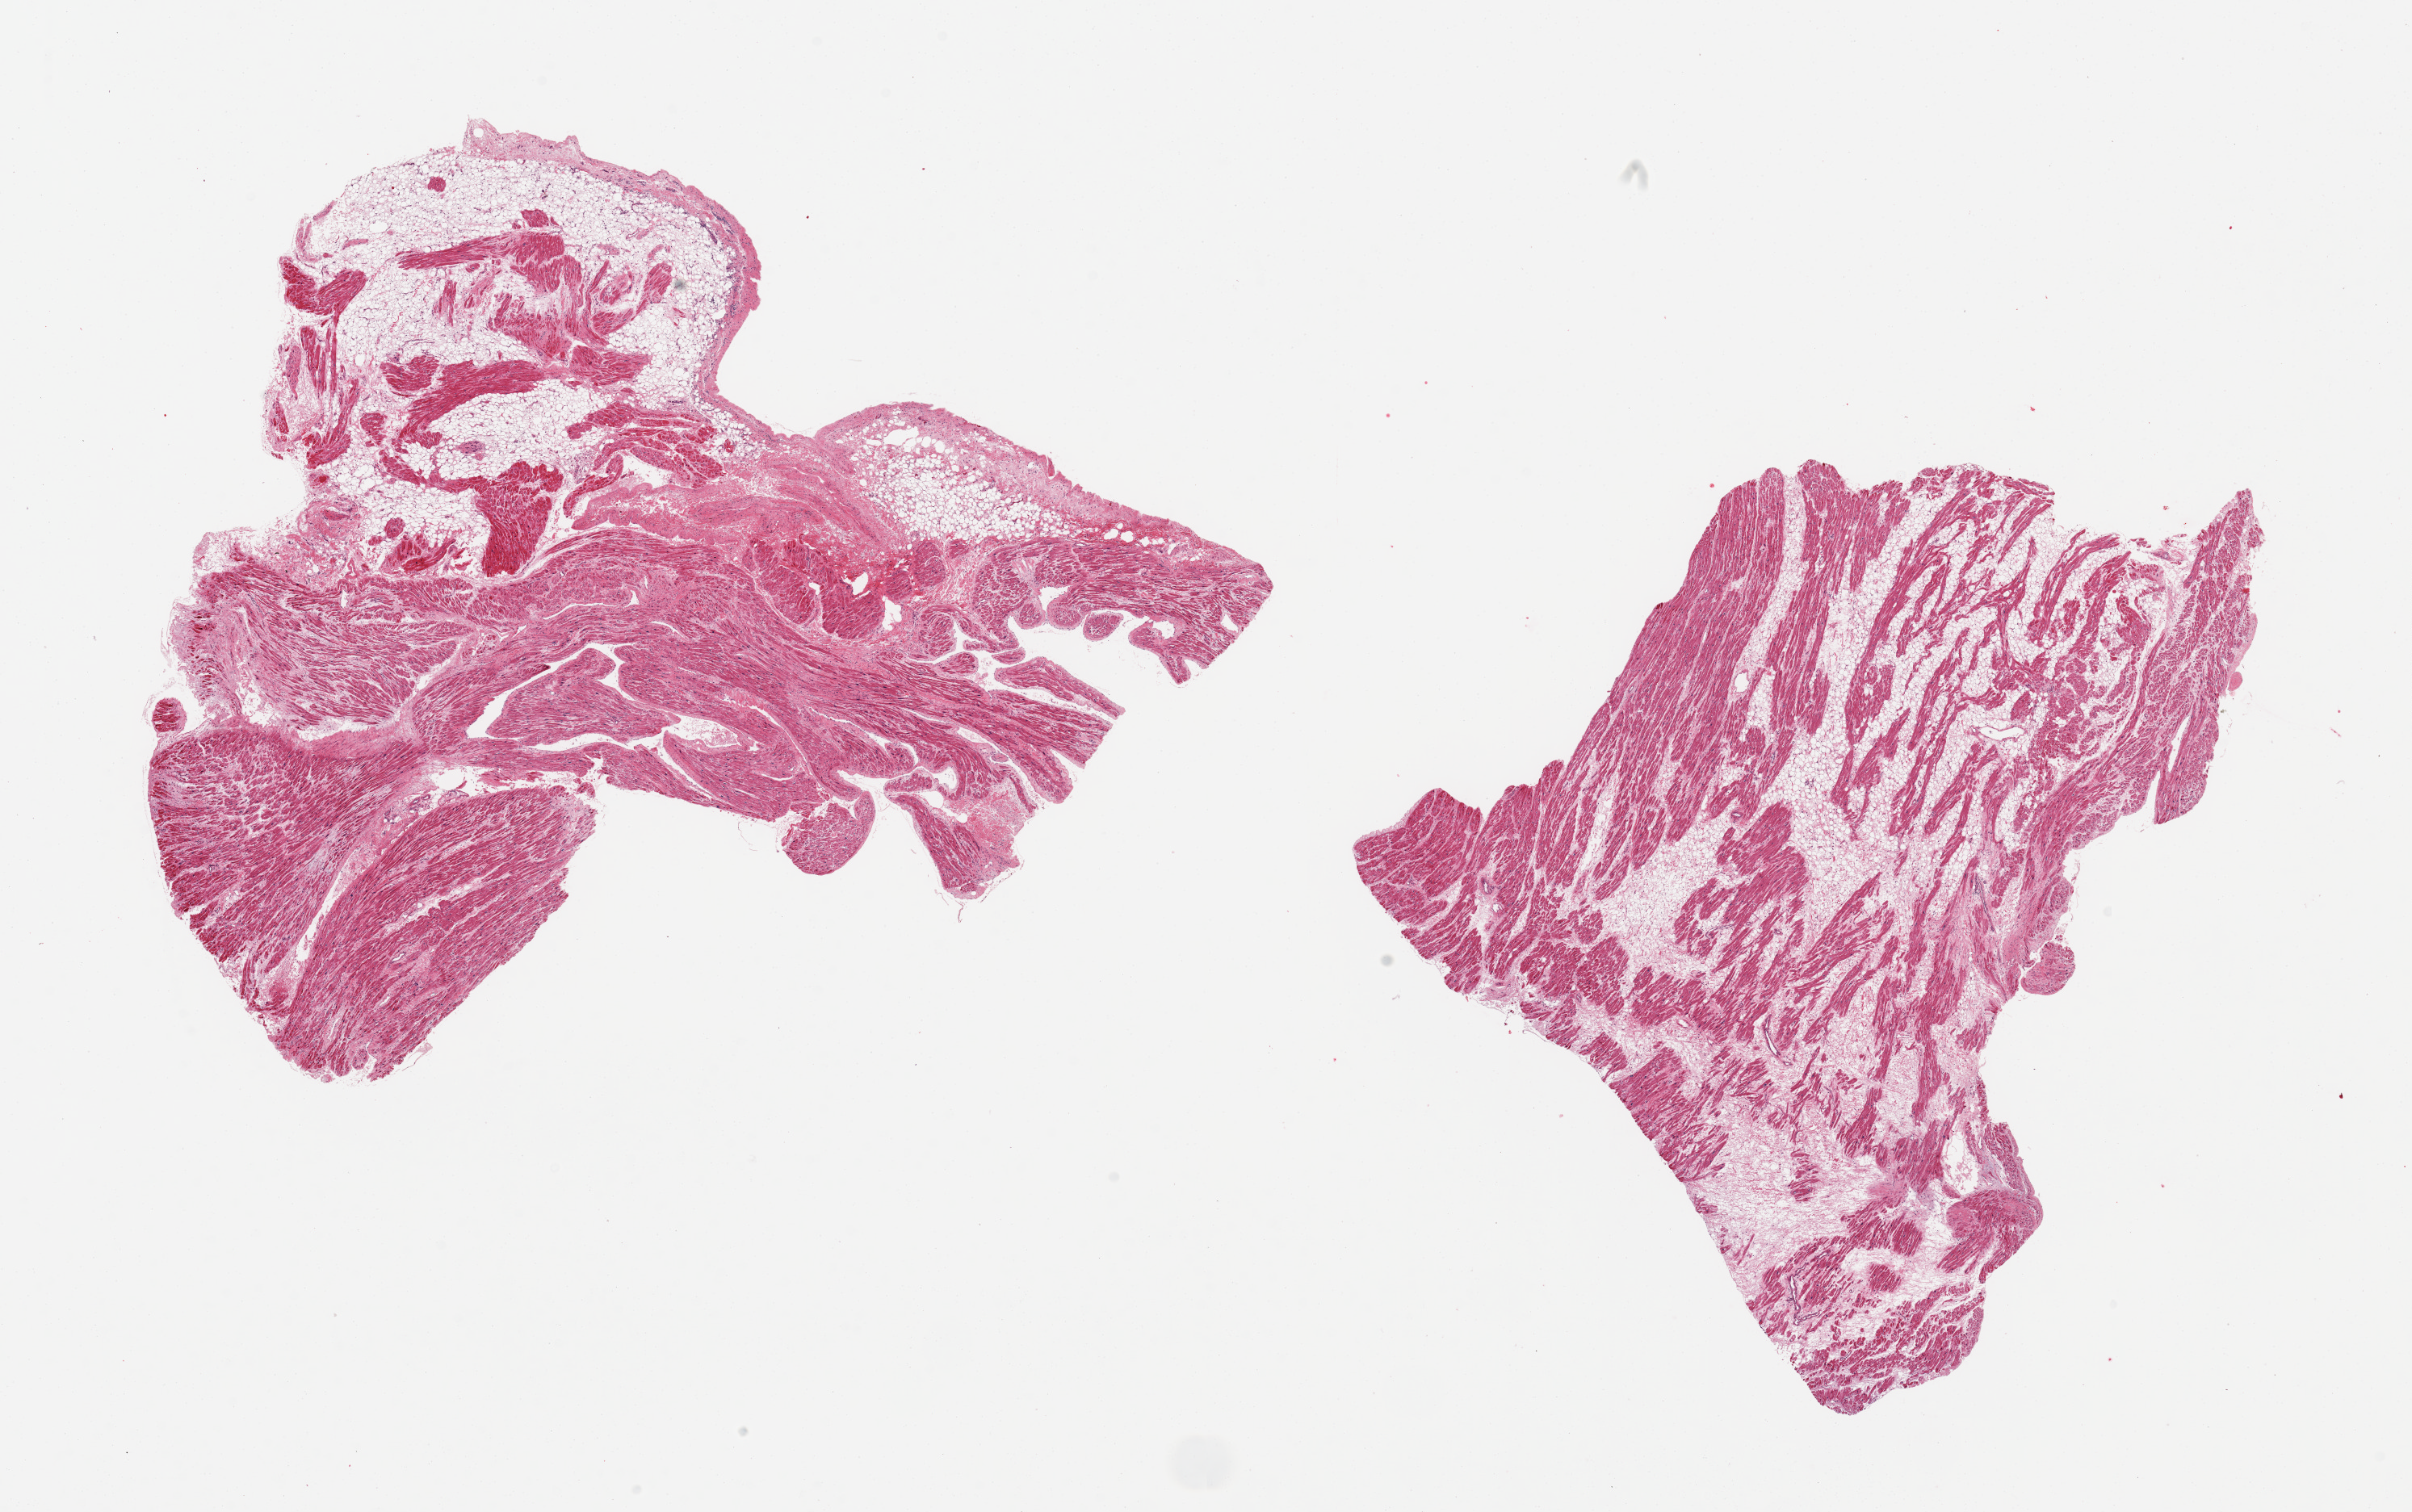
Whole-slide image, H&E stain — a low-resolution overview of the entire scanned area, about 23.6 x 14.8 mm (from a 20x scan). PAXgene-fixed paraffin-embedded (PFPE) section. Section of auricular appendage (target tissue). Tissue donor sample. Donor: female.
Reviewer comment on this tissue sample: 2 pieces cardiac atrium no abnormalities.